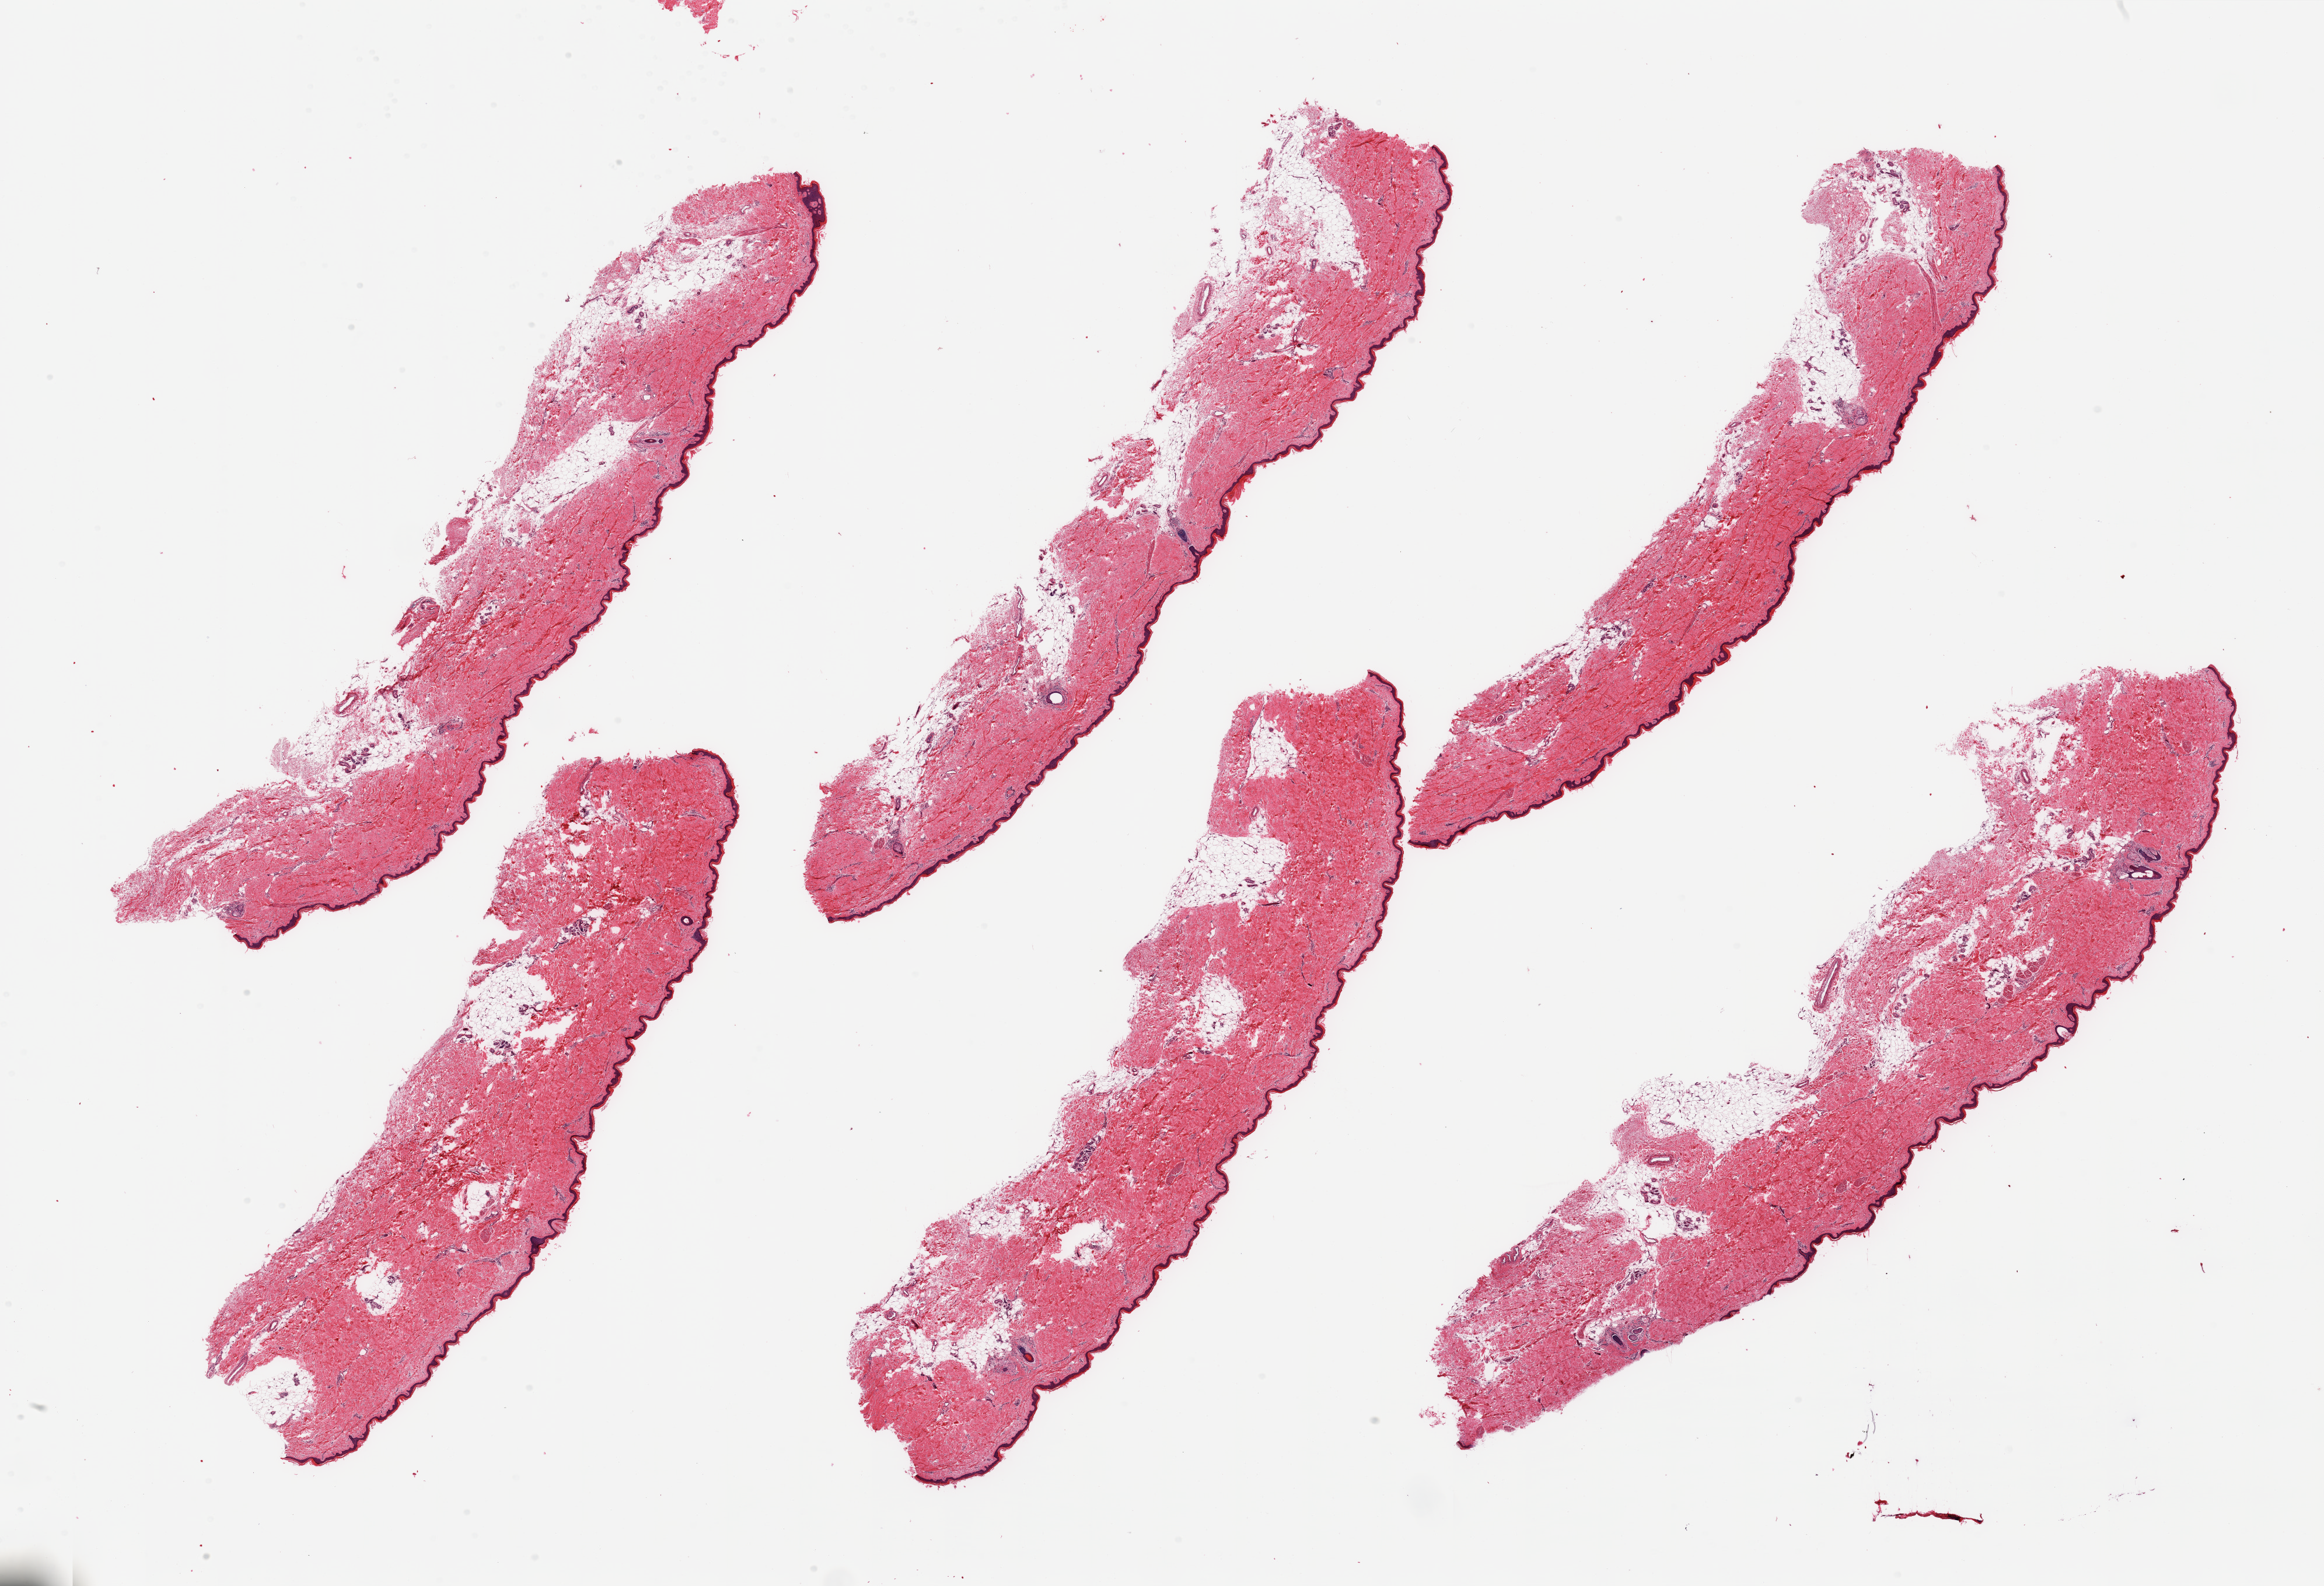
Whole-slide image, H&E stain, shown as a low-resolution overview of the whole scanned area (about 31.5 x 21.5 mm, from a 20x scan), PAXgene-fixed paraffin-embedded (PFPE) section, target tissue: skin of lower leg, tissue donor sample. Male donor.
Reviewer comment on this tissue sample: 6 pieces; ~20% to 30% internal fat; ~30 microns epidermis.